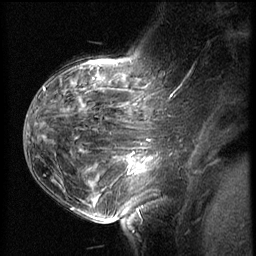
Breast MRI (dynamic contrast-enhanced), one sagittal slice. Slice 40 of 62 in the series (ordered by position). 3 images stored at this slice position (order not interpretable as contrast timing). 1.5 T. TE 4.2 ms, TR 8.9 ms. 256 × 256 image matrix, field of view 200 × 200 mm. Patient: female, 37 years. Case-level facts recorded for this patient, not image findings: setting: breast cancer imaged before/during neoadjuvant chemotherapy; receptor status: triple-negative.
Structures marked on this image (semi-automatic segmentation, software-assisted and operator-edited):
- analysis volume of interest (the breast-tissue region the enhancement analysis was run in; not a lesion): box from (x=116, y=146) to (x=168, y=203) px
- tumour enhancement mask (voxels above the 140 % enhancement threshold inside the analysis volume of interest): (x=127, y=152)–(x=153, y=175)